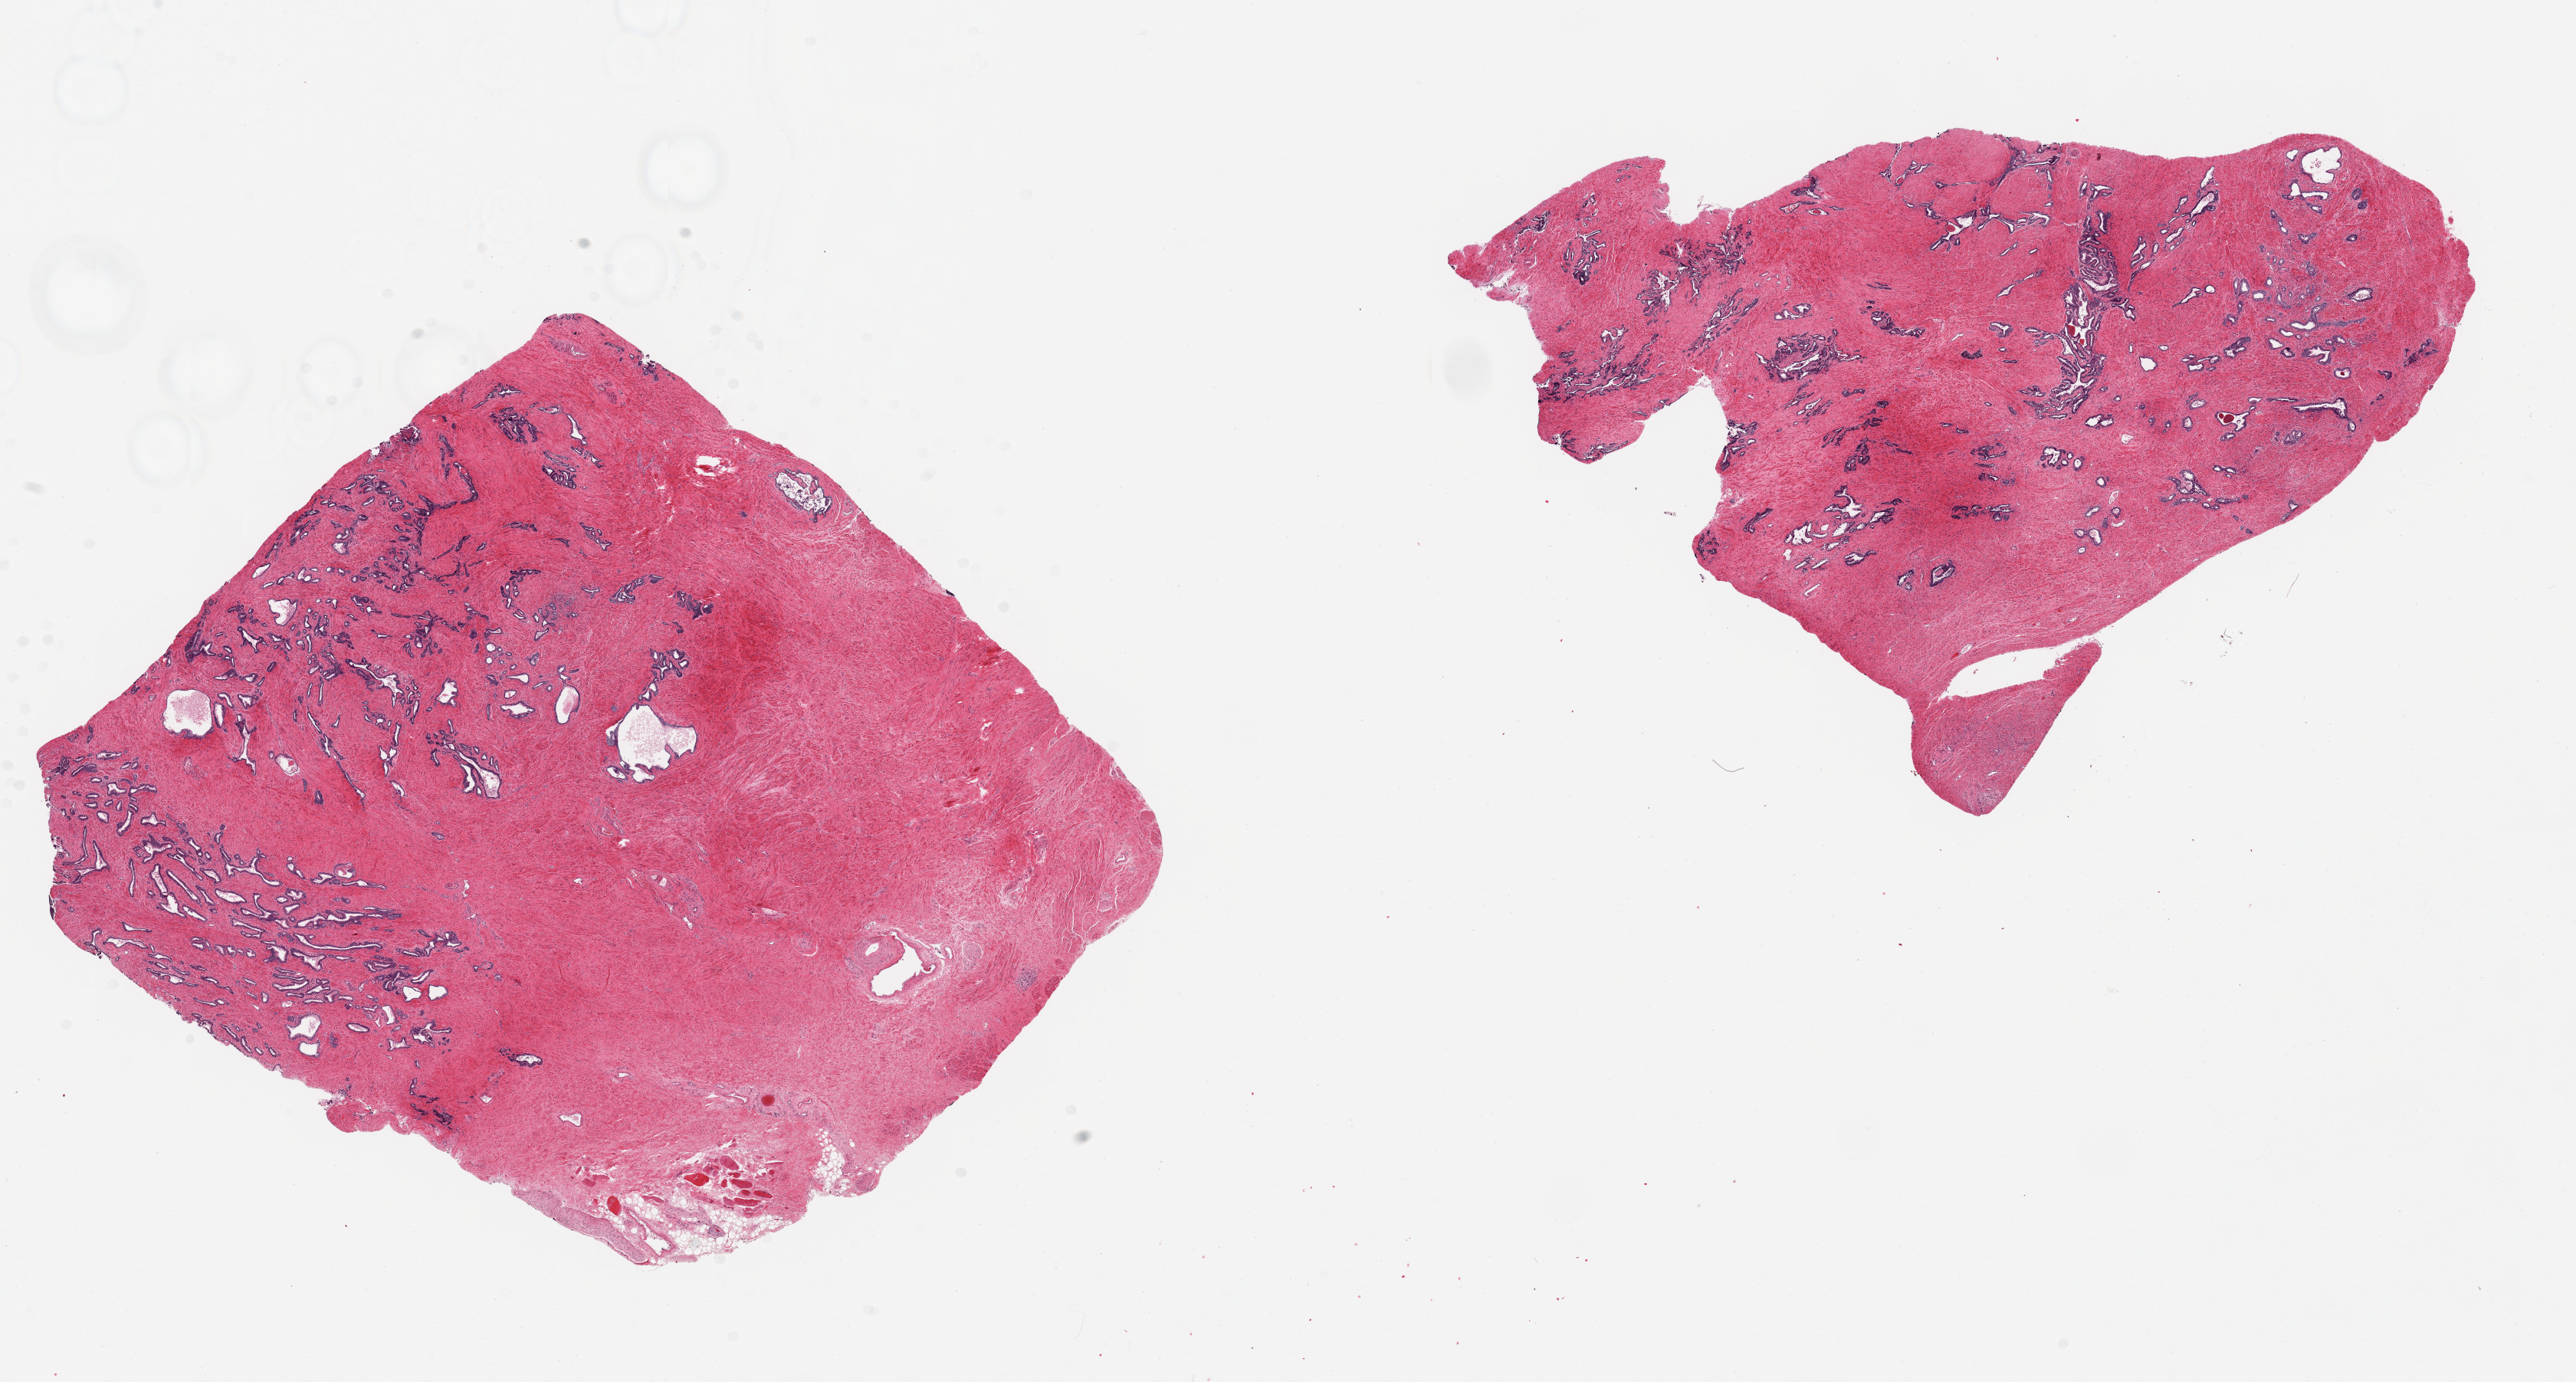
H&E whole-slide image, brightfield — whole scanned area (about 26.6 x 14.3 mm, acquisition: 20x scan) shown as a low-resolution overview; PAXgene-fixed, paraffin-embedded tissue; target tissue: prostate; donor tissue sample. Donor sex: male.
Reviewer comment on this tissue sample: 2 pieces; abundant stroma in better condition than glands.